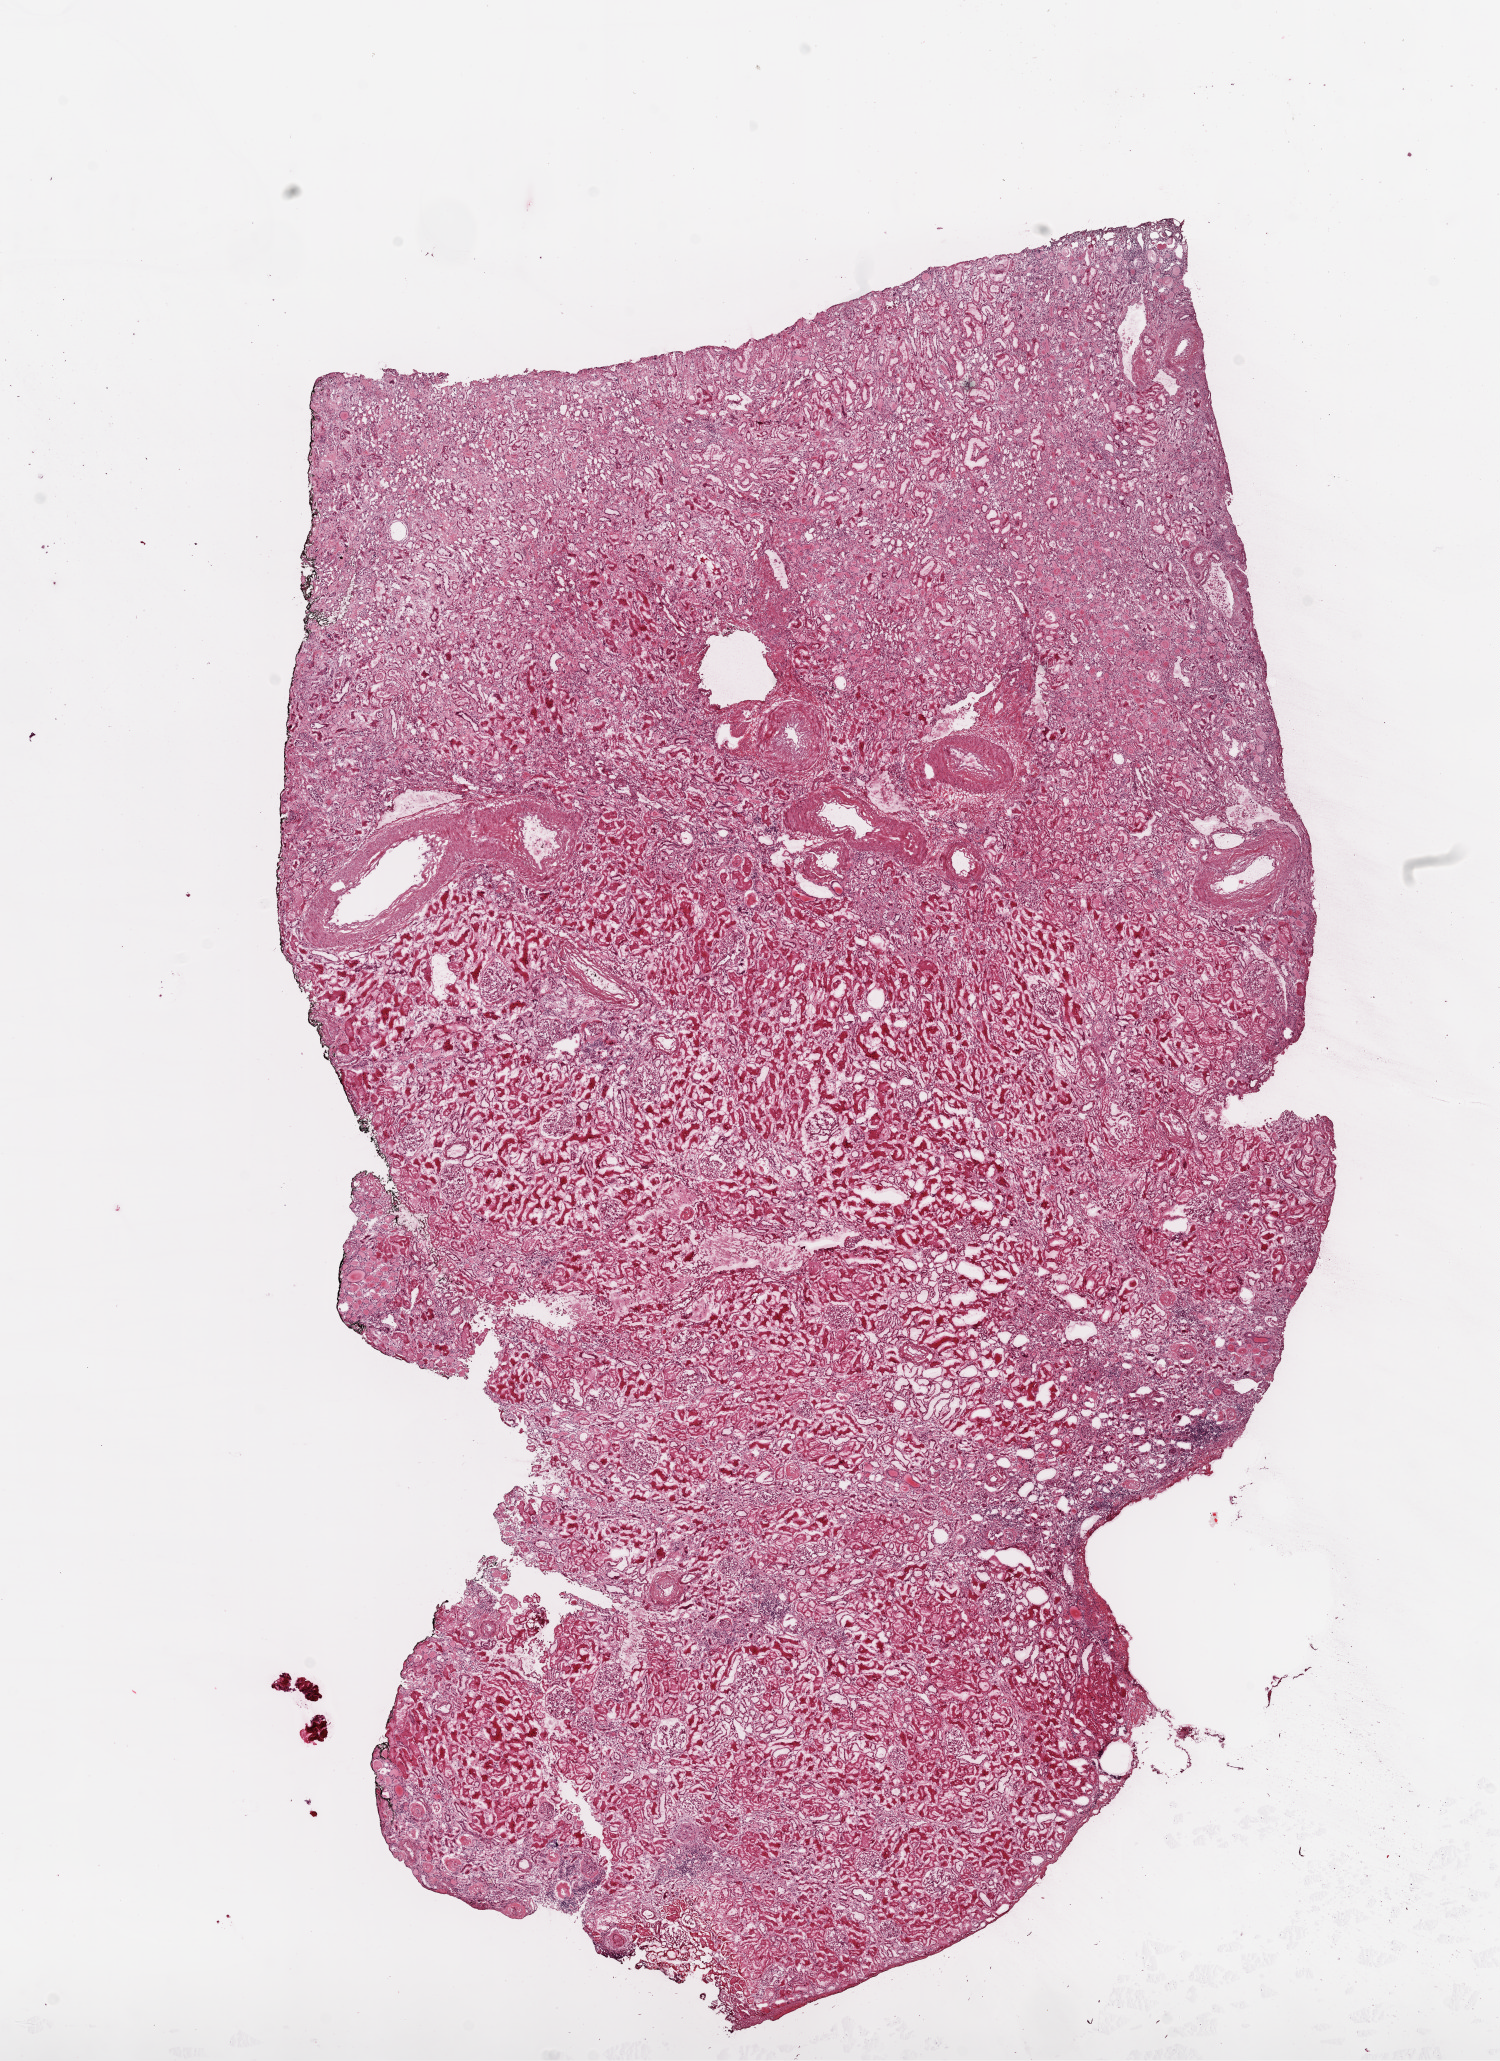
Hematoxylin and eosin (H&E) stained whole-slide image, a low-resolution overview of the entire scanned area, about 12.0 x 16.5 mm (acquisition: 20x scan). Frozen section from the top of the tissue portion. Sample: solid tissue normal (non-tumour tissue), kidney. Patient: female, age at initial diagnosis 79 years.
This section: solid tissue normal (non-tumour) sample from the same patient. Patient diagnosis: Clear cell adenocarcinoma, NOS.